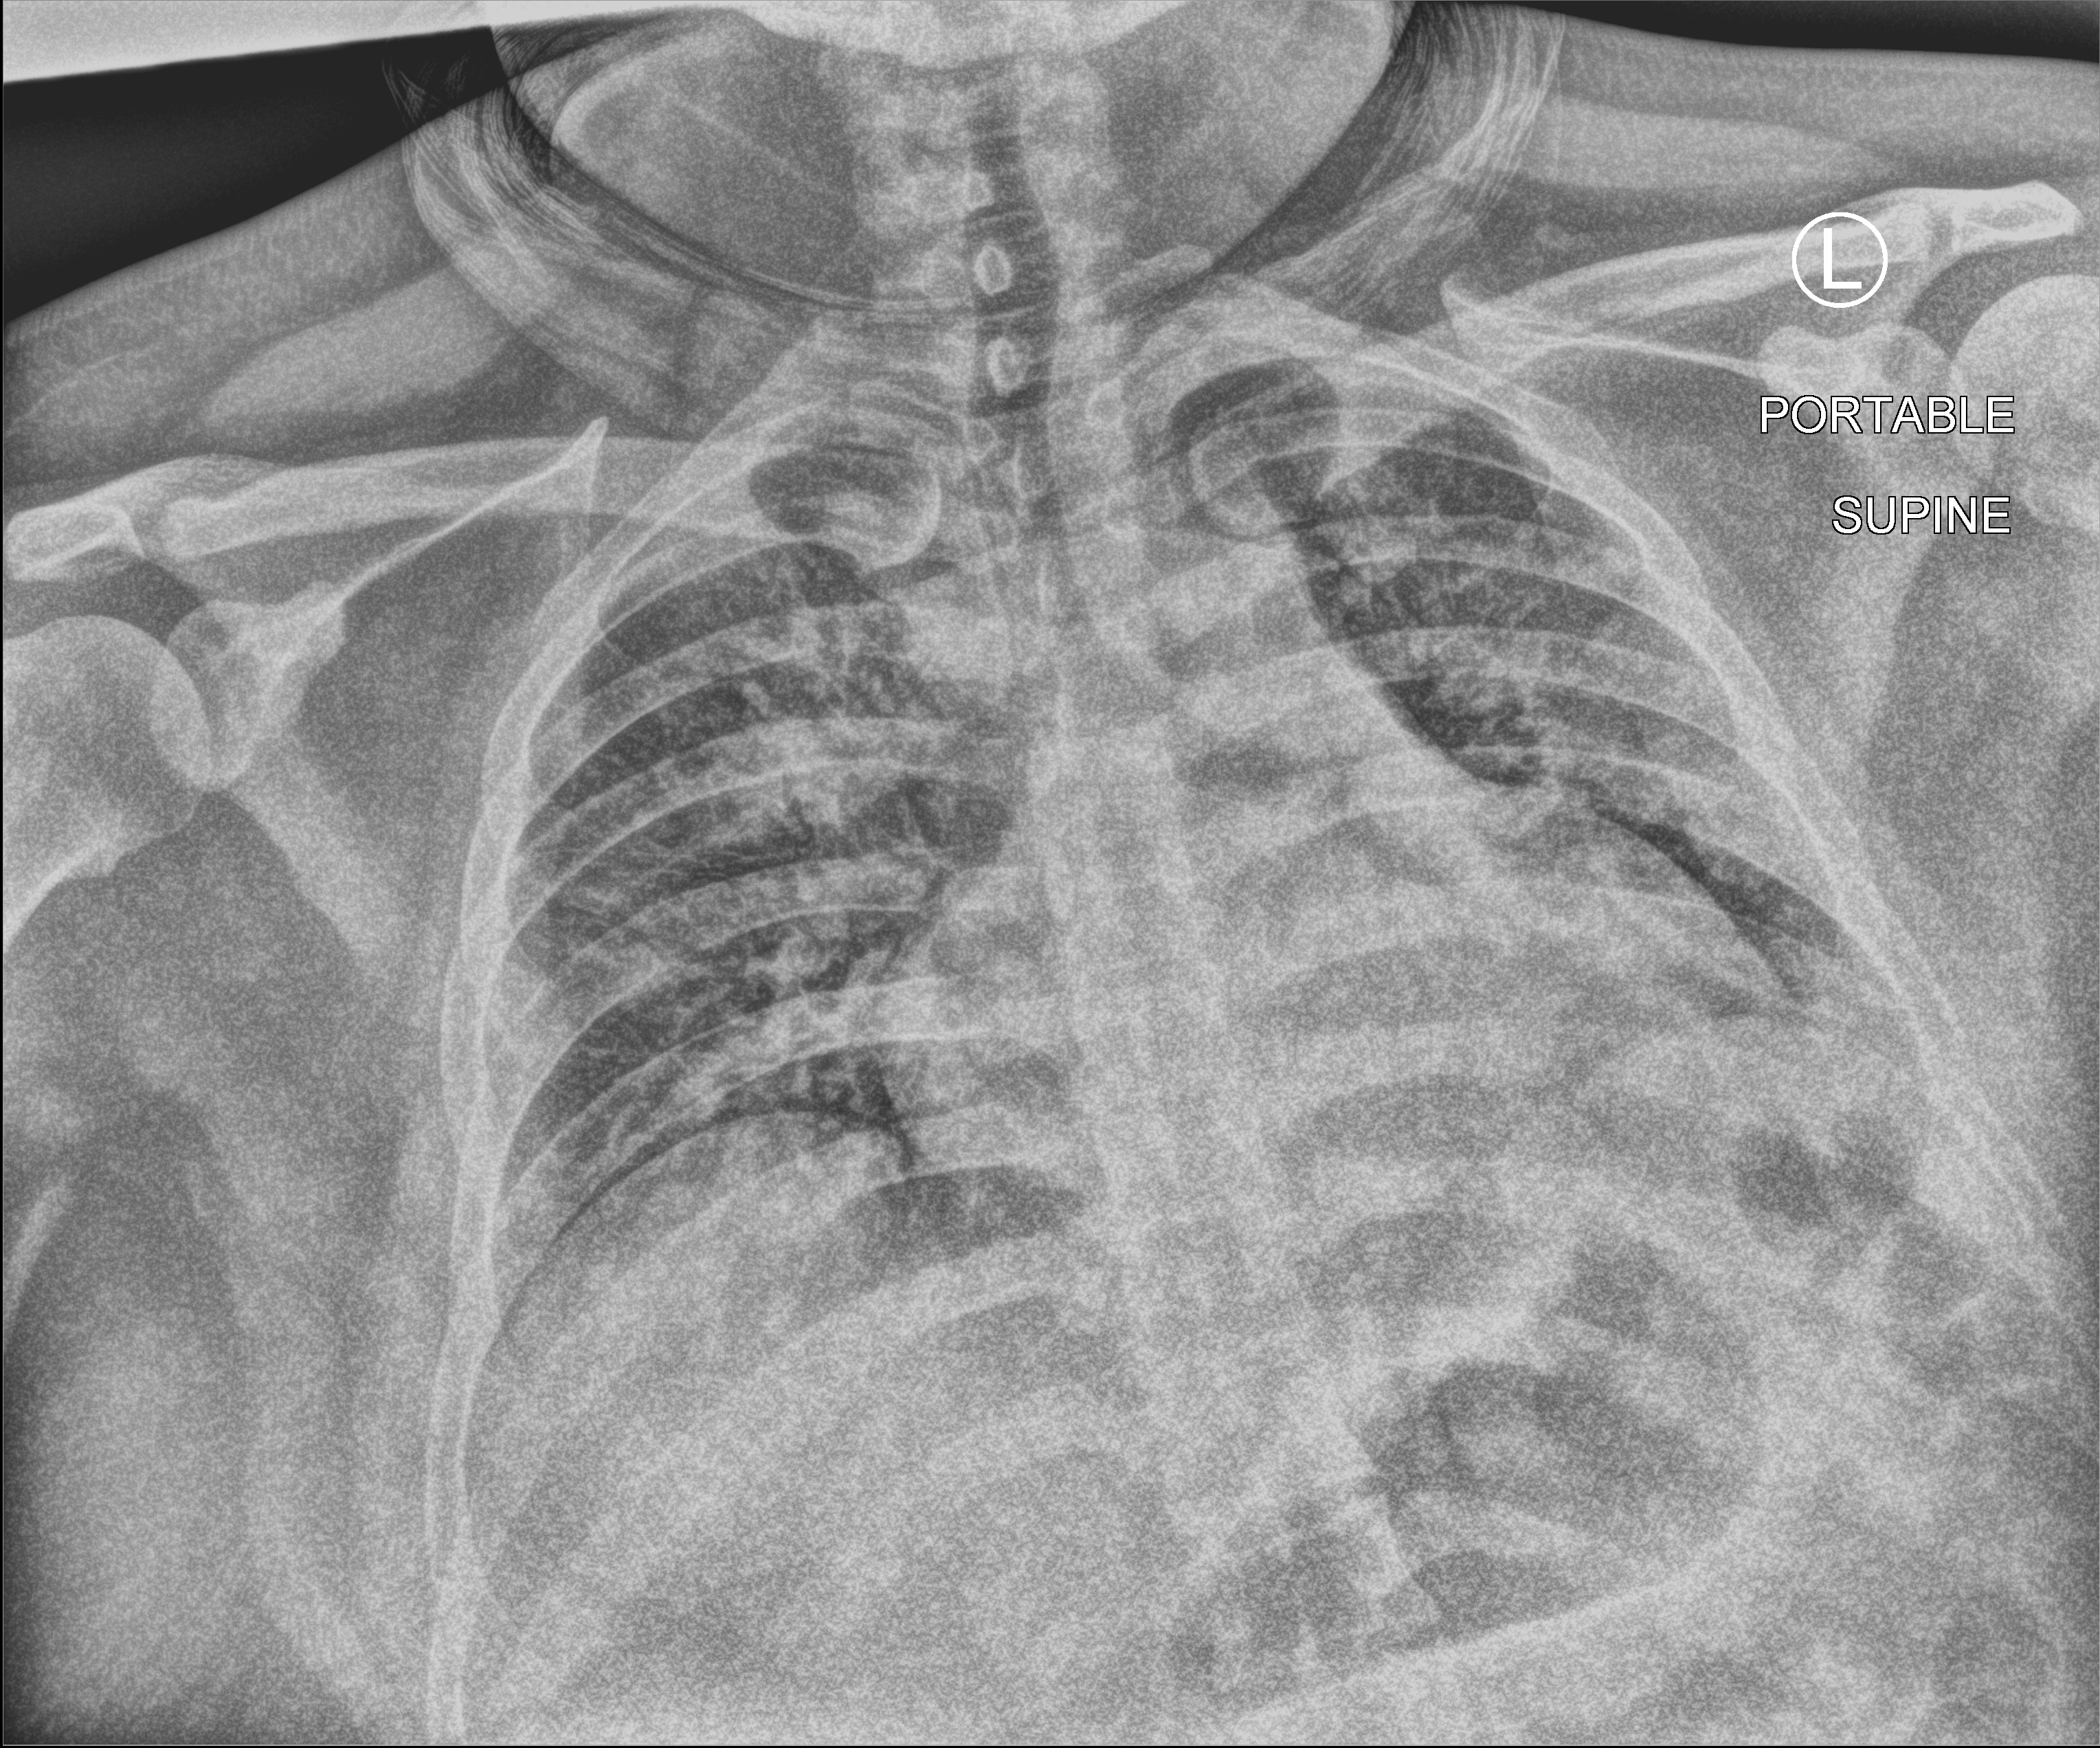
Portable chest radiograph, anteroposterior (AP) projection. Patient hospitalised with COVID-19; male, aged 18–59 years.
From the hospital-stay record, not from the radiograph (when in the stay this image was taken is not recorded):
- chronic kidney disease (admission record): no